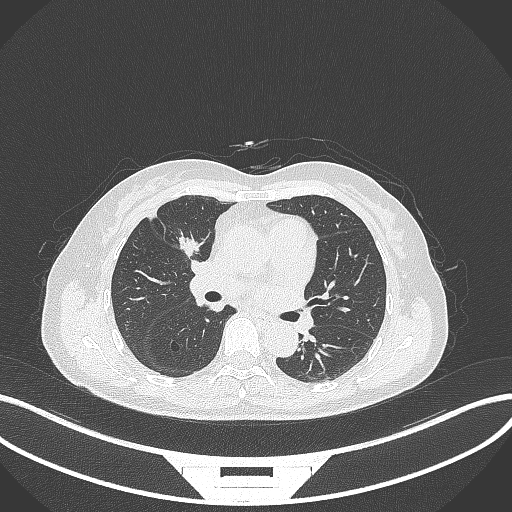
Chest CT, one axial slice; slice 165 of 284 in the series (ordered by position); 120 kVp; lung window (W 1500 / L -600 HU); 1 mm slice thickness; 512 × 512 image matrix, field of view 400 × 400 mm. Female patient, age 51 years. Case-level facts recorded for this patient, not image findings: clinical TNM (as recorded): T1c N0 M0.
Outlined on this slice (bounding box drawn by a radiologist):
- lung tumour (recorded histology: adenocarcinoma): bounding box (x1, y1, x2, y2) in pixels: (176, 233, 202, 263)